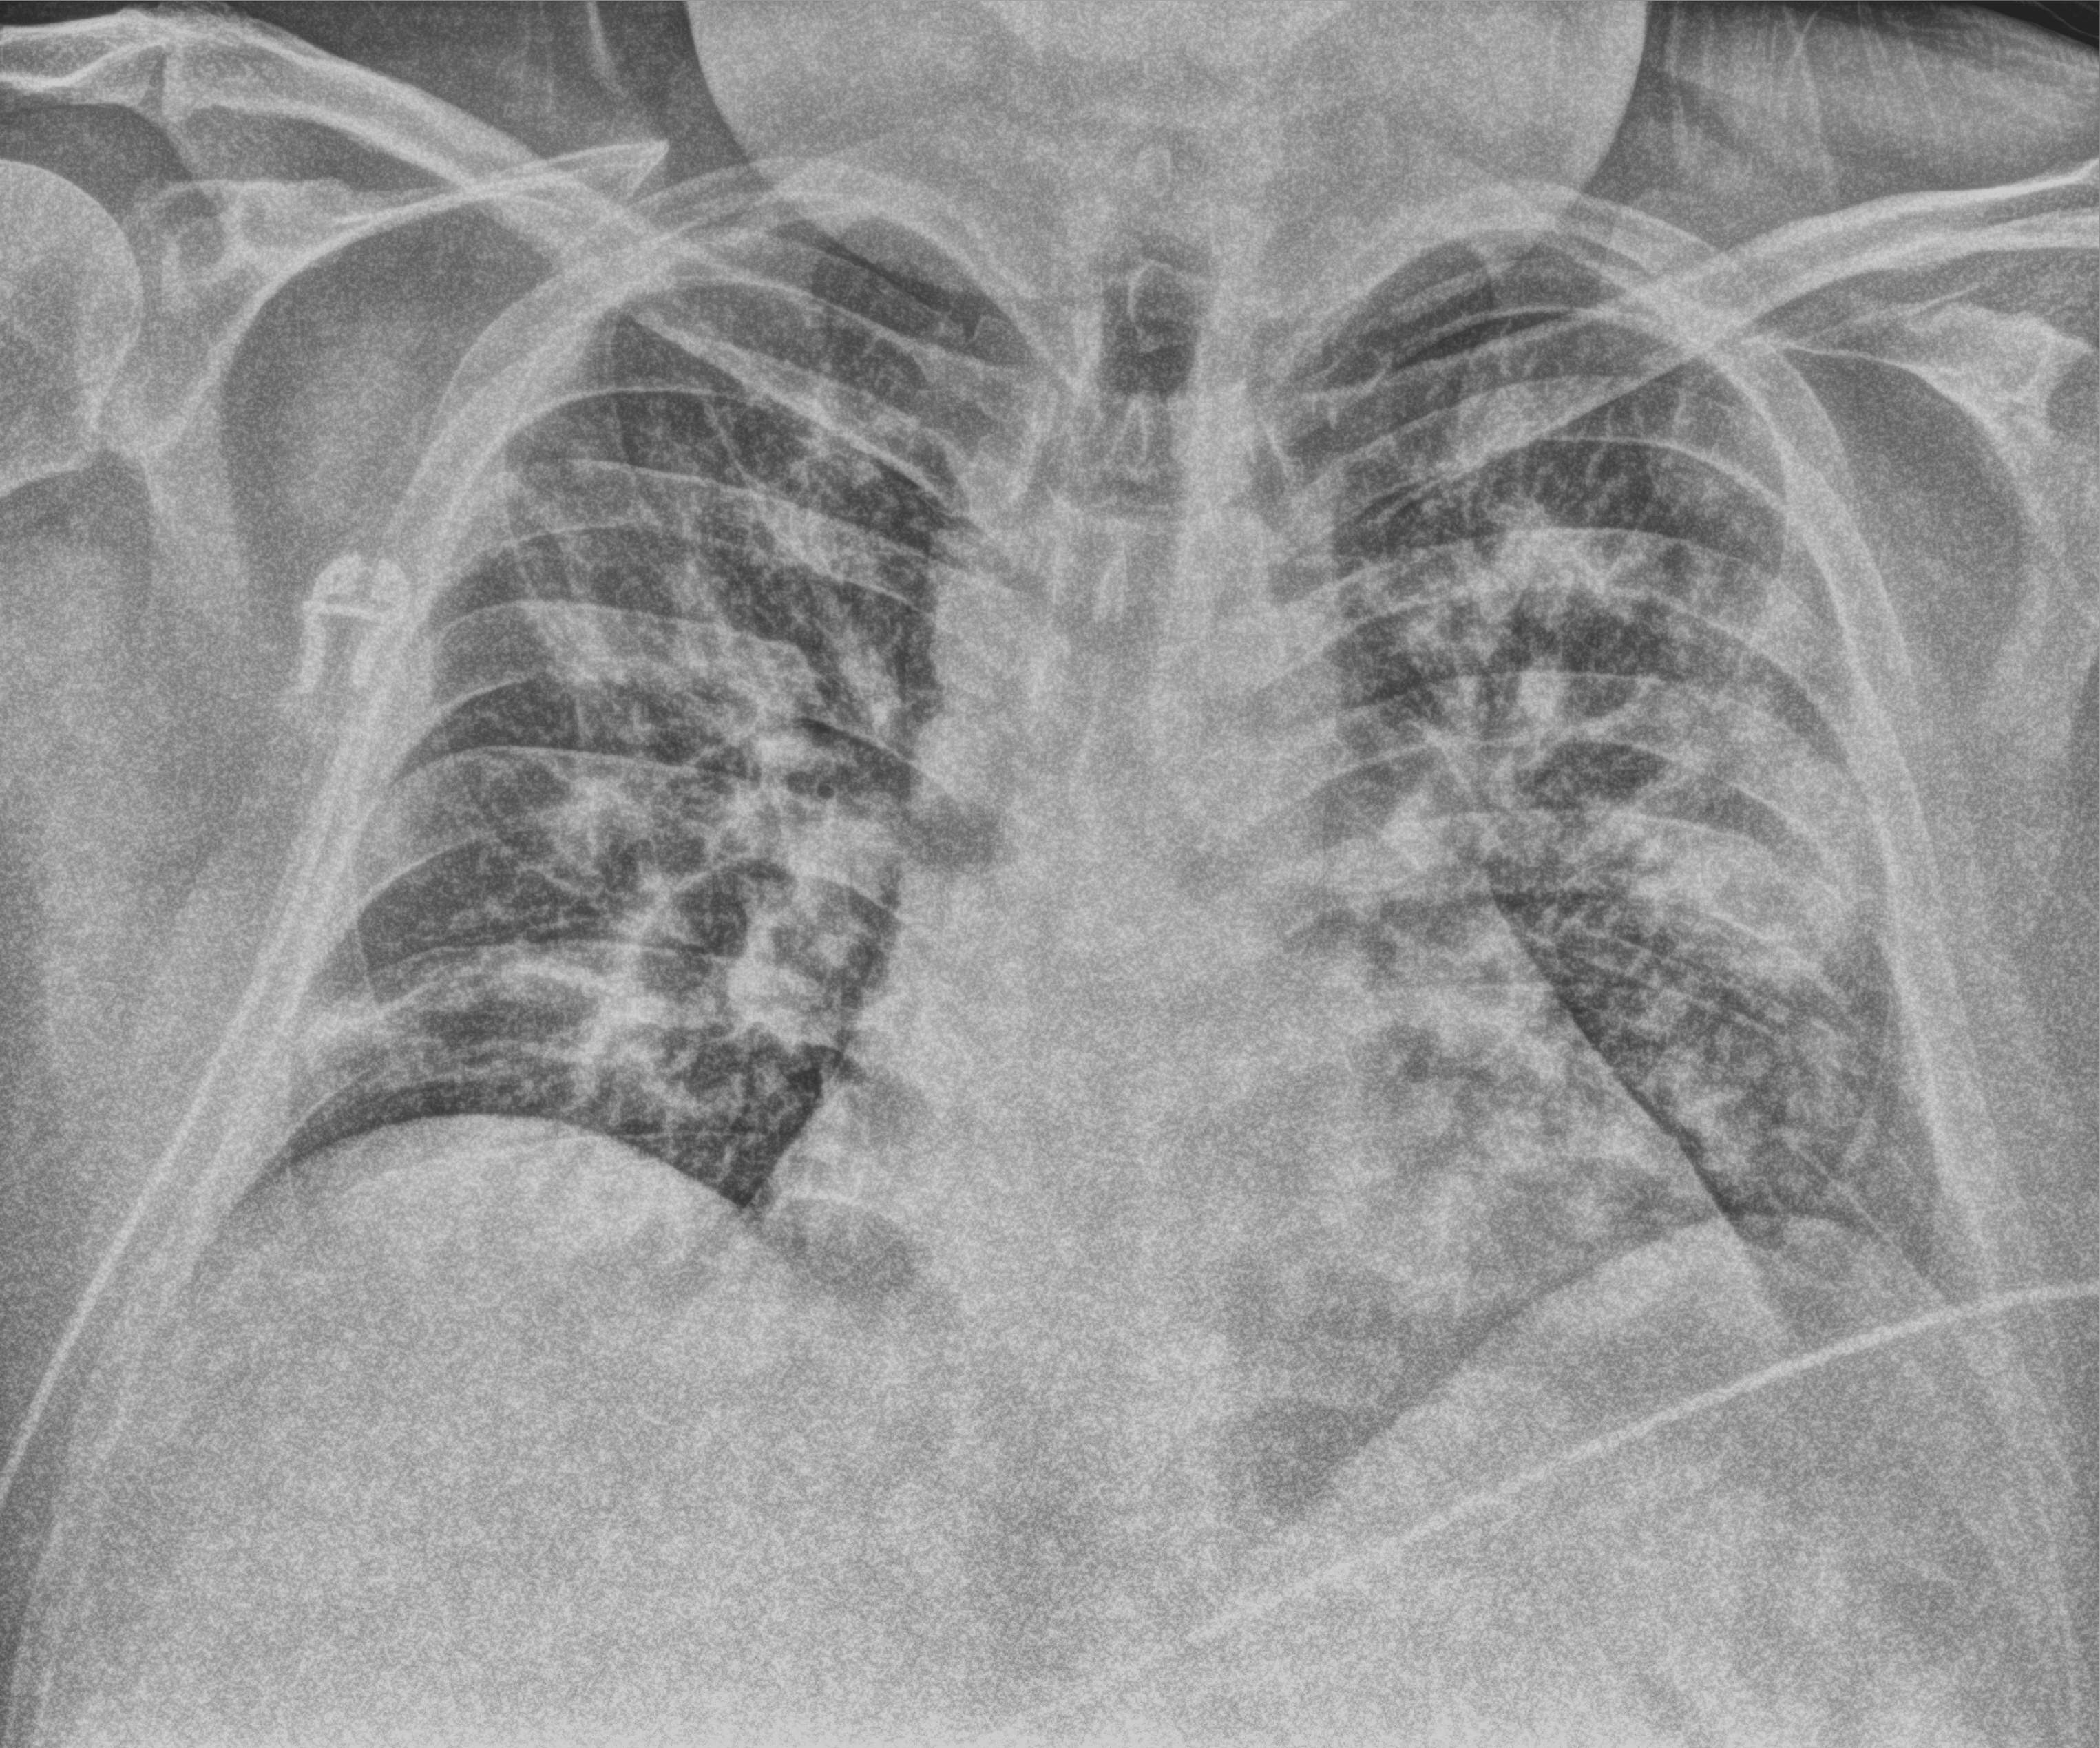
Chest X-ray (portable), anteroposterior (AP) projection. Patient hospitalised with COVID-19; male, aged 18–59 years.
Hospital-stay facts (about this admission, not read from this image; timing relative to this image not recorded): admitted to intensive care during this hospital stay: yes; mechanically ventilated during this hospital stay: no.